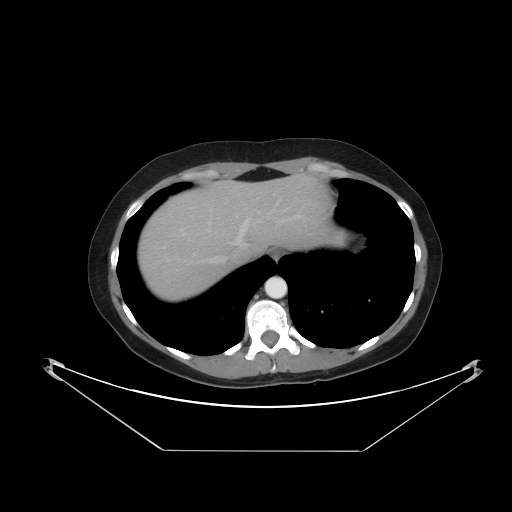
Contrast-enhanced abdominal CT, one axial slice; slice 40 of 48 in the series (ordered by position); 120 kVp; intravenous contrast given; soft-tissue window (W 400 / L 40 HU); 5 mm slice thickness; 512 × 512 image matrix, field of view 482 × 482 mm. Female patient, age 38 years. Case-level facts recorded for this patient, not image findings: diagnosis: colorectal cancer liver metastases, imaged before liver resection; multiple liver metastases: yes; largest metastasis: 2.5 cm; disease in both lobes: no.
Annotated regions visible in this slice (expert manual segmentation):
- hepatic veins: bounding box (x1, y1, x2, y2) in pixels: (208, 210, 300, 262)
- liver: (138, 177, 330, 301)
- planned liver remnant (the part of the liver to remain after resection): (206, 177, 329, 253)